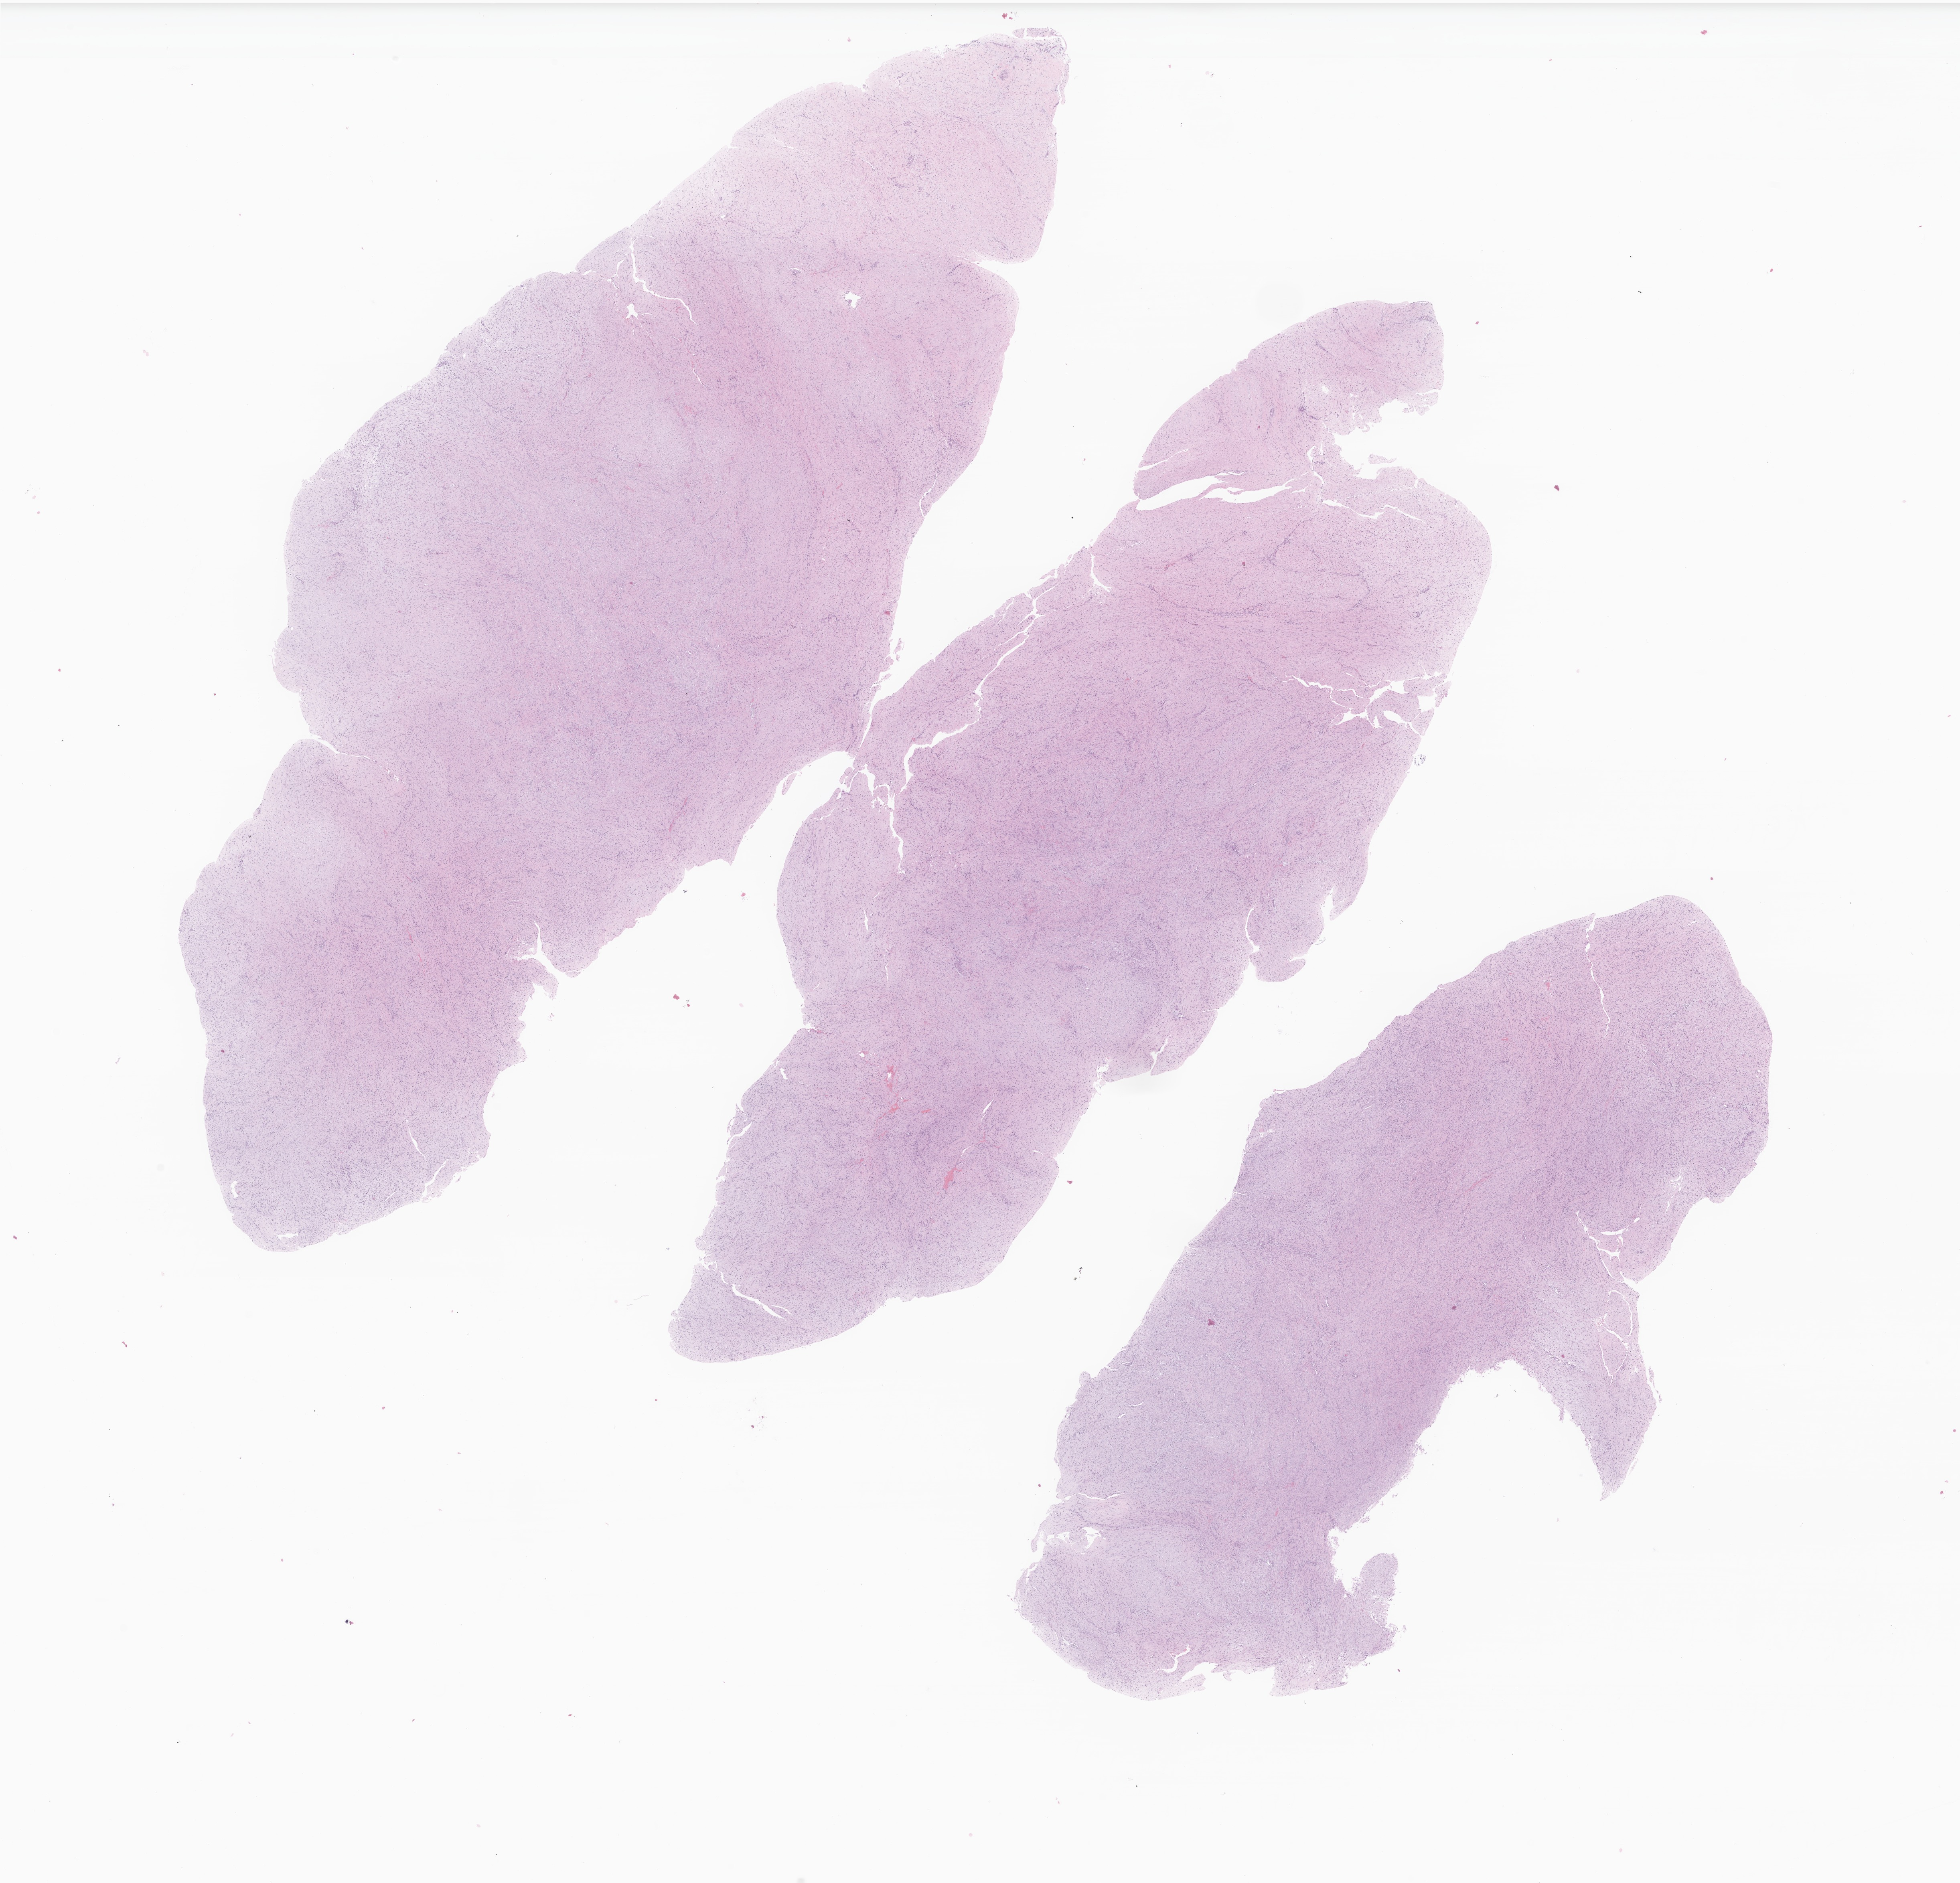
Whole-slide image, H&E stain of tumor tissue from the head and neck, shown as a low-resolution overview of the whole scanned area (about 20.6 x 19.8 mm); formalin-fixed, paraffin-embedded (FFPE) tissue. Male patient, age 171 months (14 years 3 months).
Recorded diagnosis: Aggressive fibromatosis.